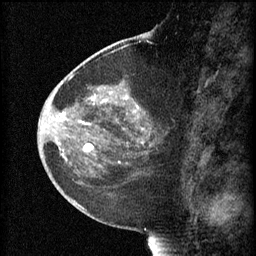
Breast MRI (dynamic contrast-enhanced), one sagittal slice. Slice 29 of 60 in the series (ordered by position). 3 images stored at this slice position (order not interpretable as contrast timing). 1.5 T. TE 4.2 ms, TR 8.2 ms. 2 mm slice thickness. 256 × 256 image matrix, field of view 180 × 180 mm. Female patient, age 44 years.
Structures marked on this image (semi-automatically segmented with operator editing):
- analysis volume of interest (the breast-tissue region the enhancement analysis was run in; not a lesion): box from (x=73, y=82) to (x=169, y=165) px
- tumour enhancement mask (voxels above the 70 % enhancement threshold inside the analysis volume of interest): (x=80, y=94)–(x=145, y=163)